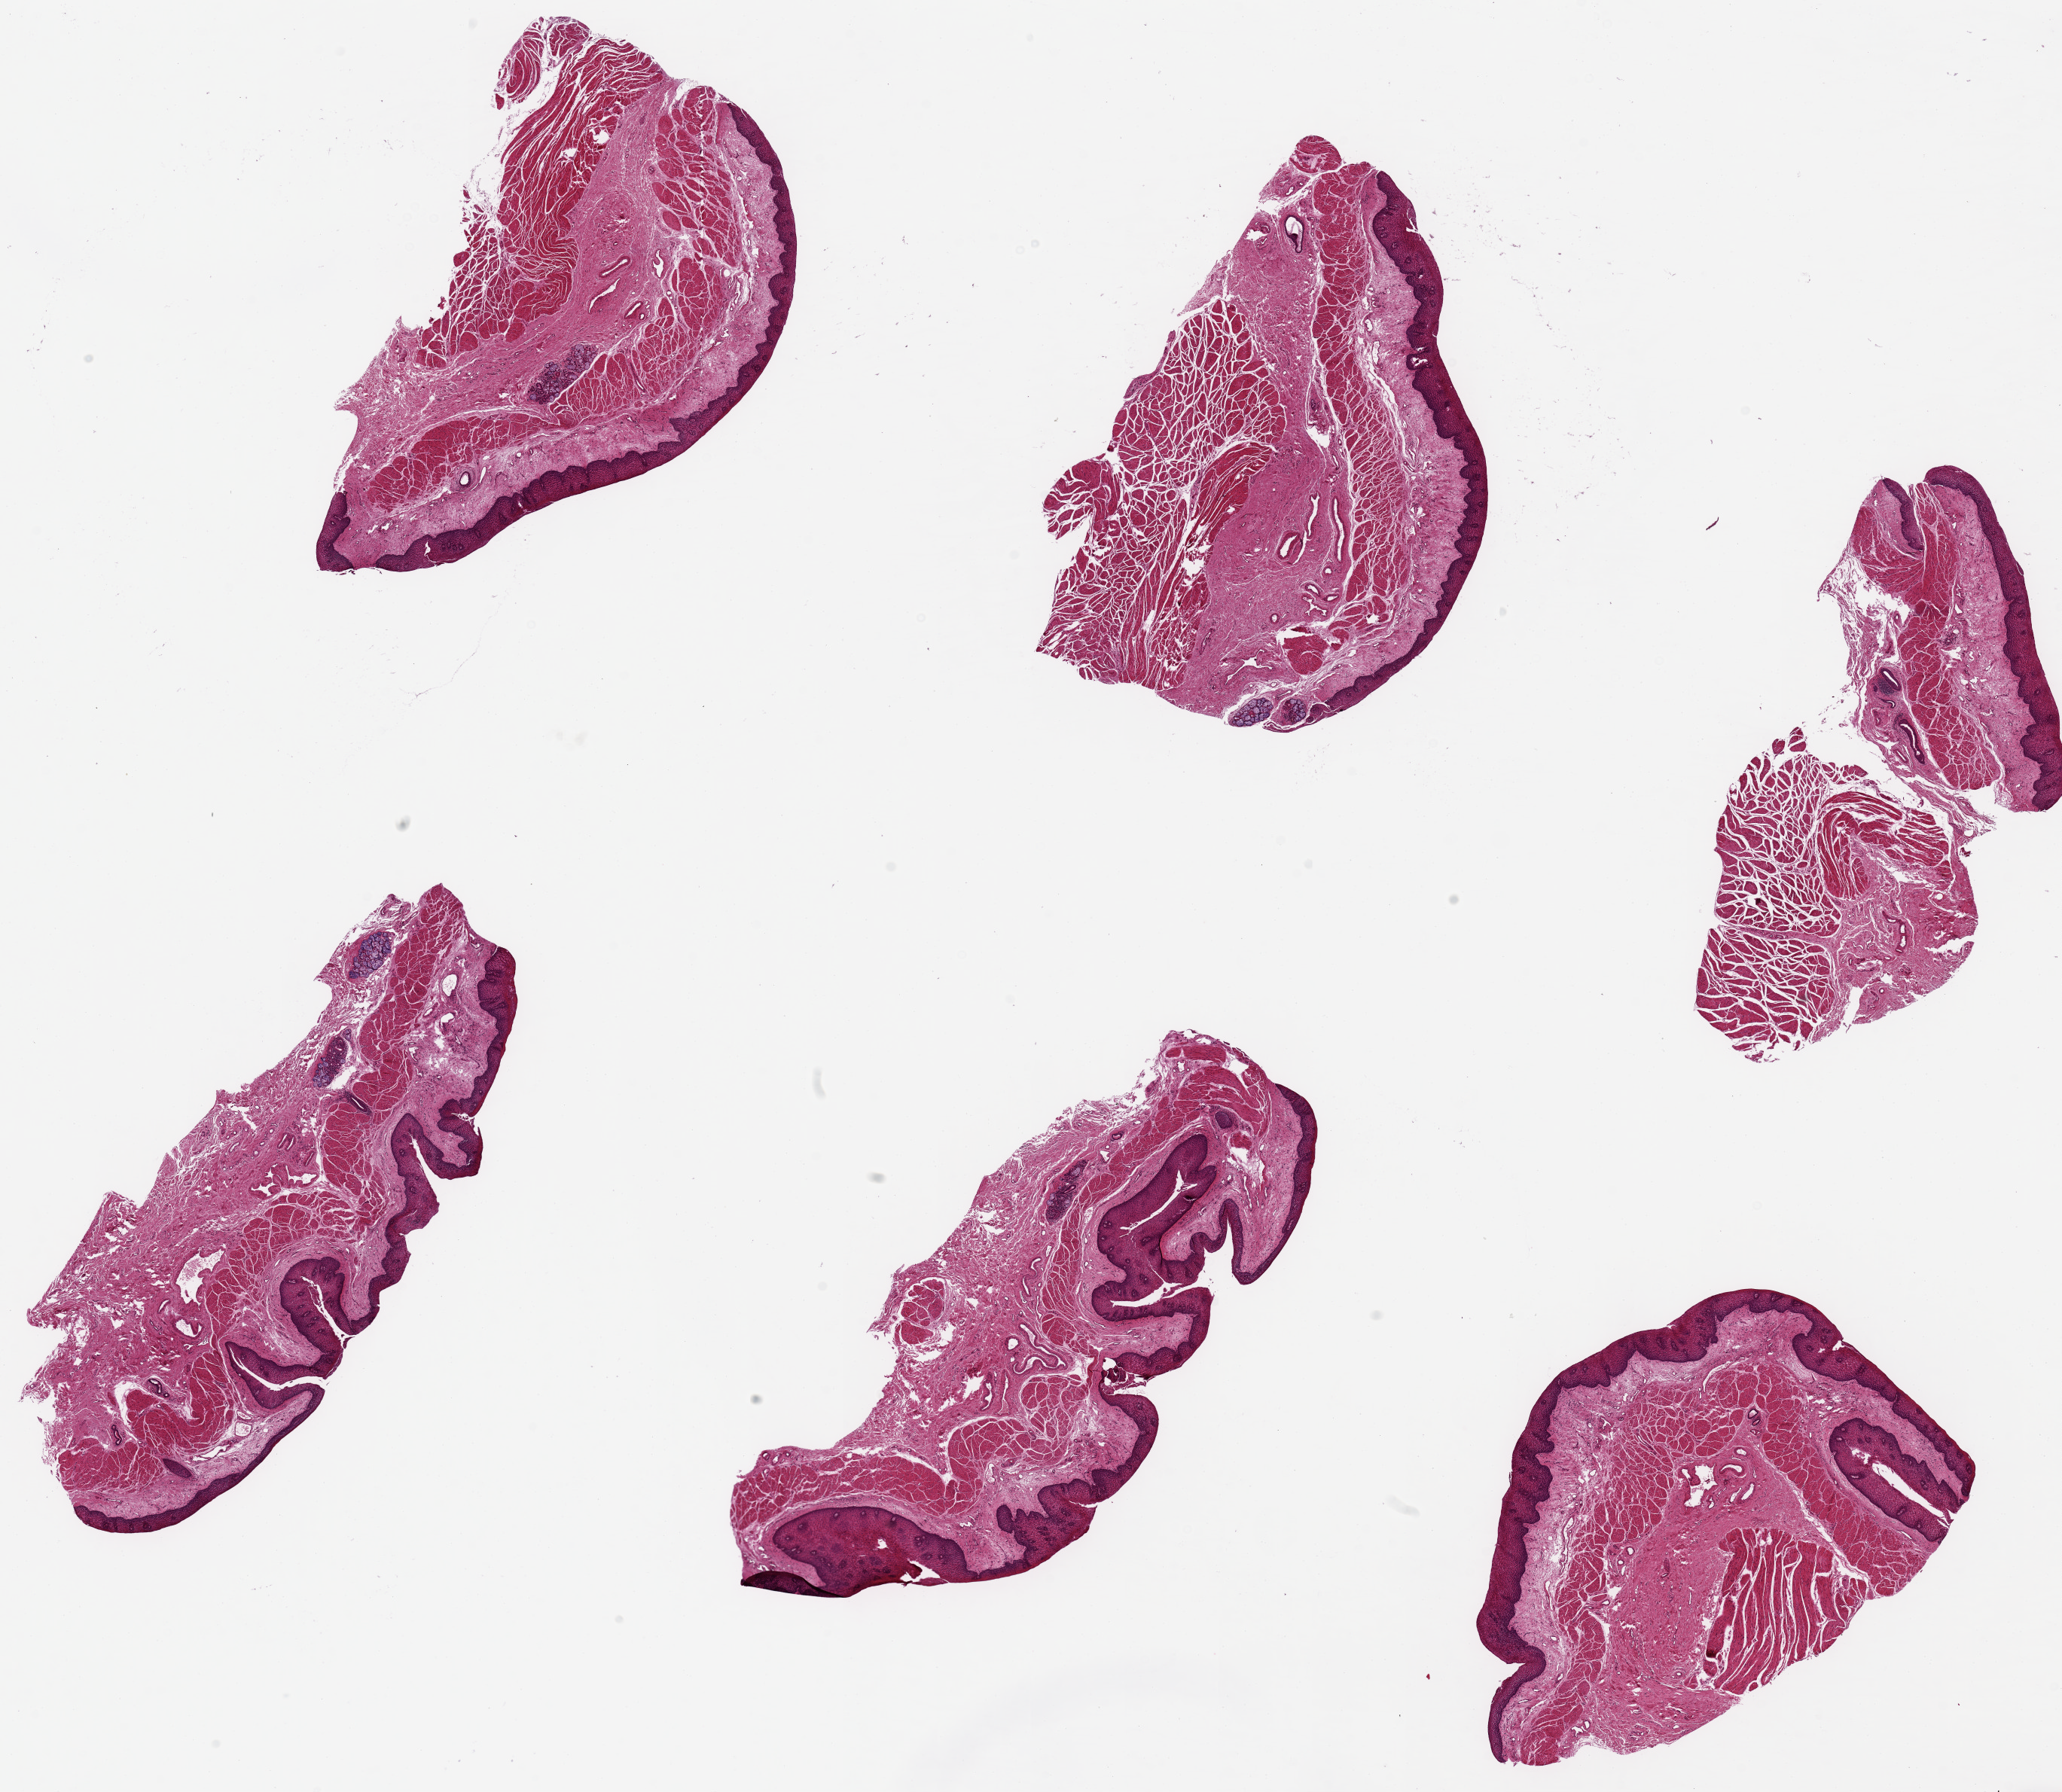
Digitized H&E-stained section, brightfield, shown as a low-resolution overview of the whole scanned area (about 21.7 x 18.8 mm, slide scanned at 20x); PAXgene-fixed, paraffin-embedded tissue; section of esophageal mucous membrane (target tissue); tissue donor sample.
Pathologist's review note for this sample: 6 pieces, up to 7x3mm; well preserved mucosa with prominent muscularis mucosae and fibrotic submucosa; most have parts of UNWANTED muscularis propria (see image).